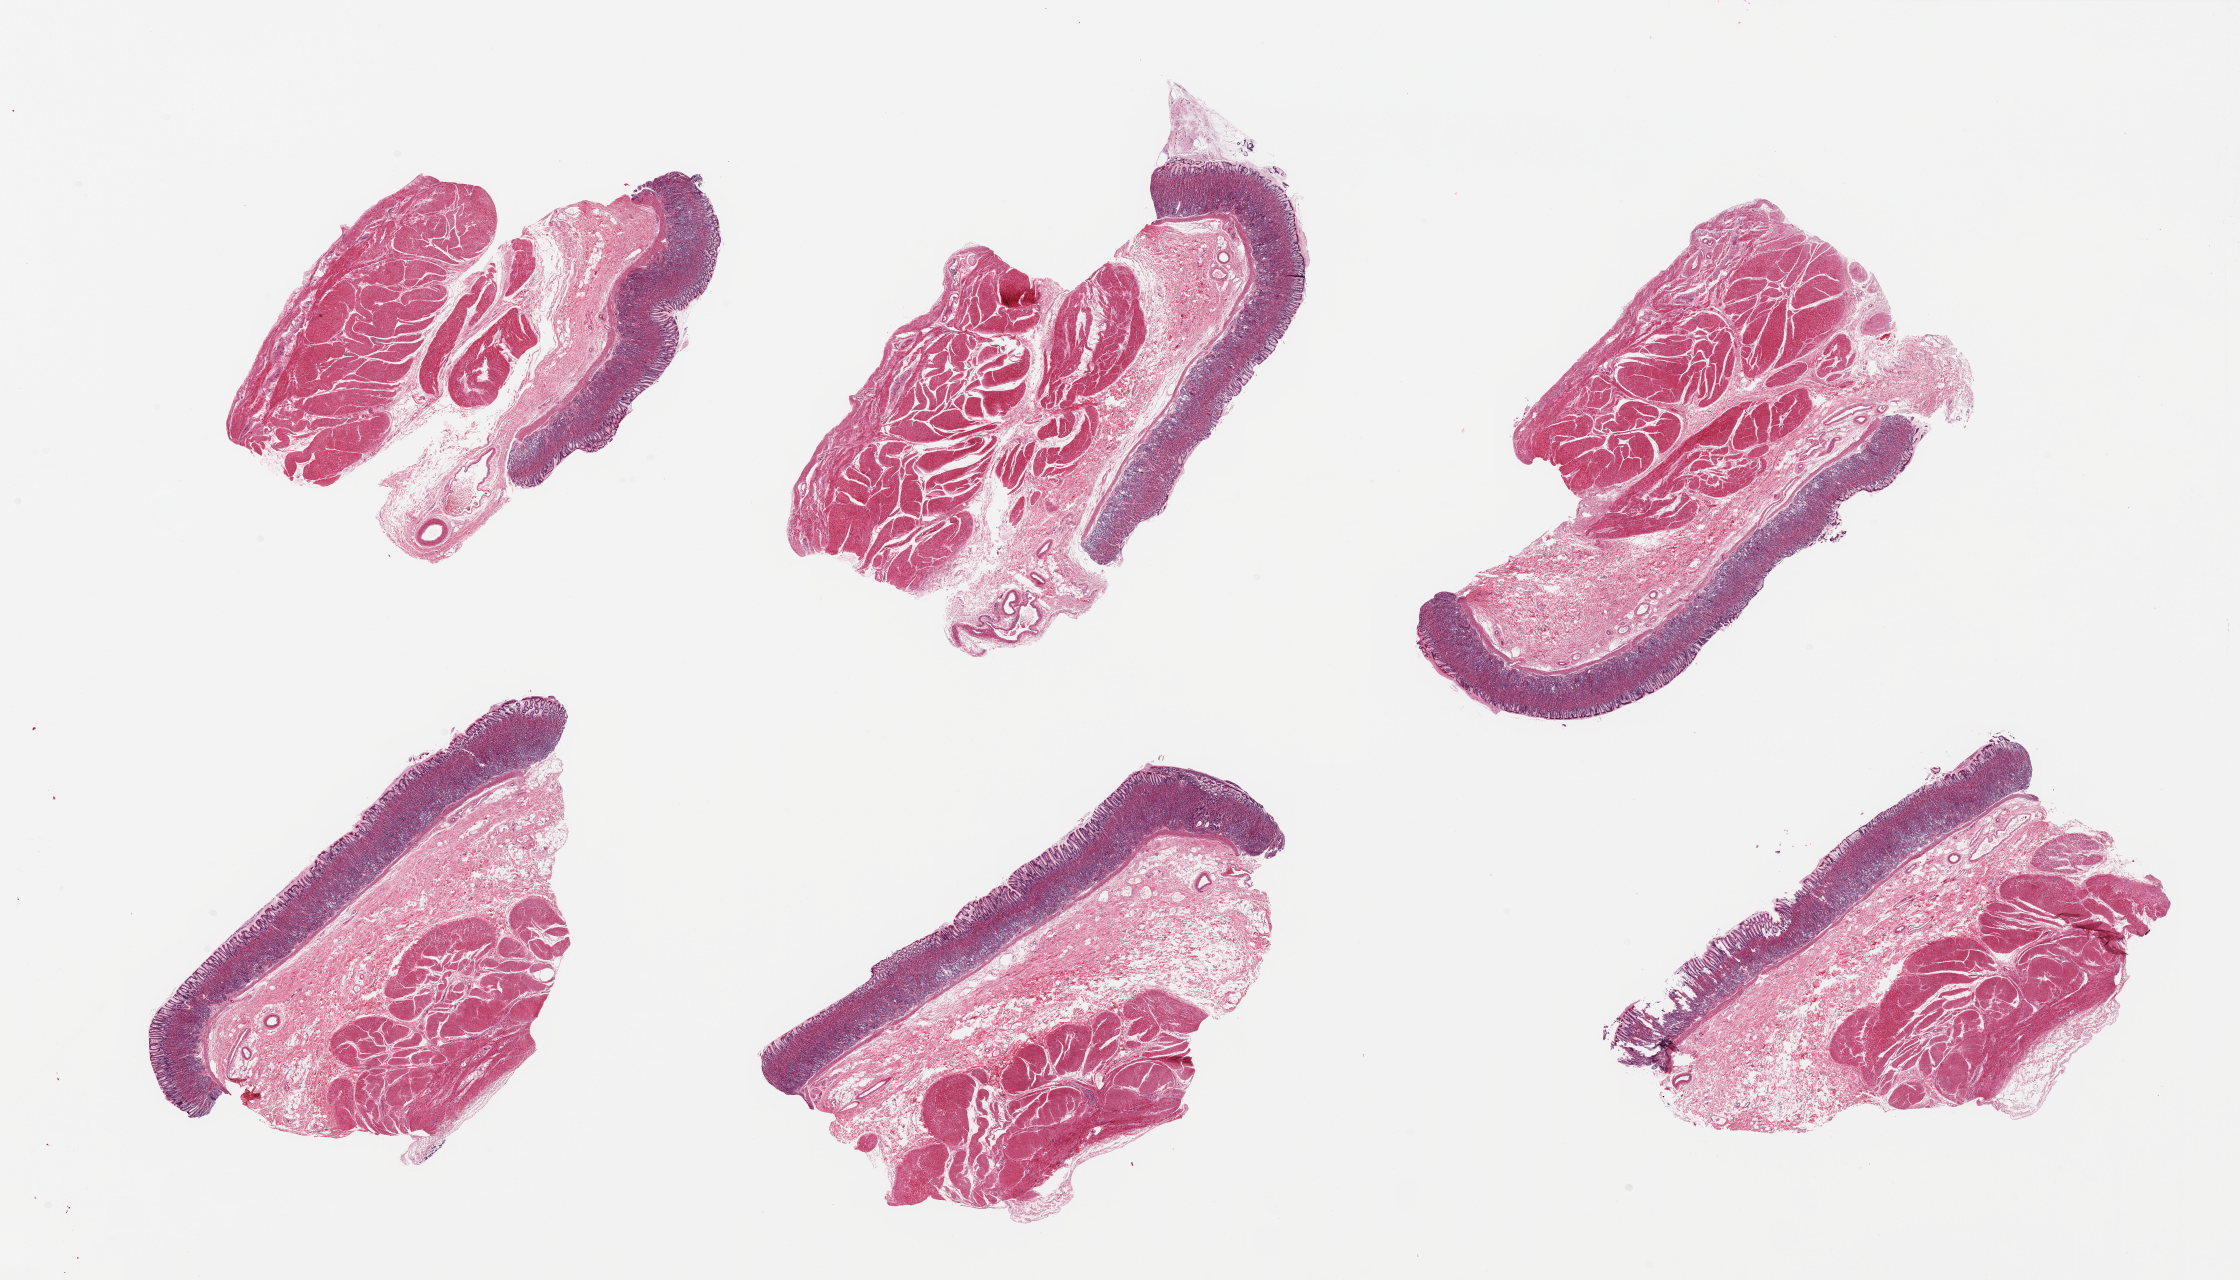
Digitized haematoxylin and eosin-stained section, a low-resolution overview of the entire scanned area, about 35.4 x 20.3 mm. PAXgene-fixed paraffin-embedded (PFPE) section. Section of stomach (target tissue). Tissue donor sample. Male donor.
Review note (as recorded): 6 pieces, superb preservation, mucosa up to ~1mm, 15-20% thickness.